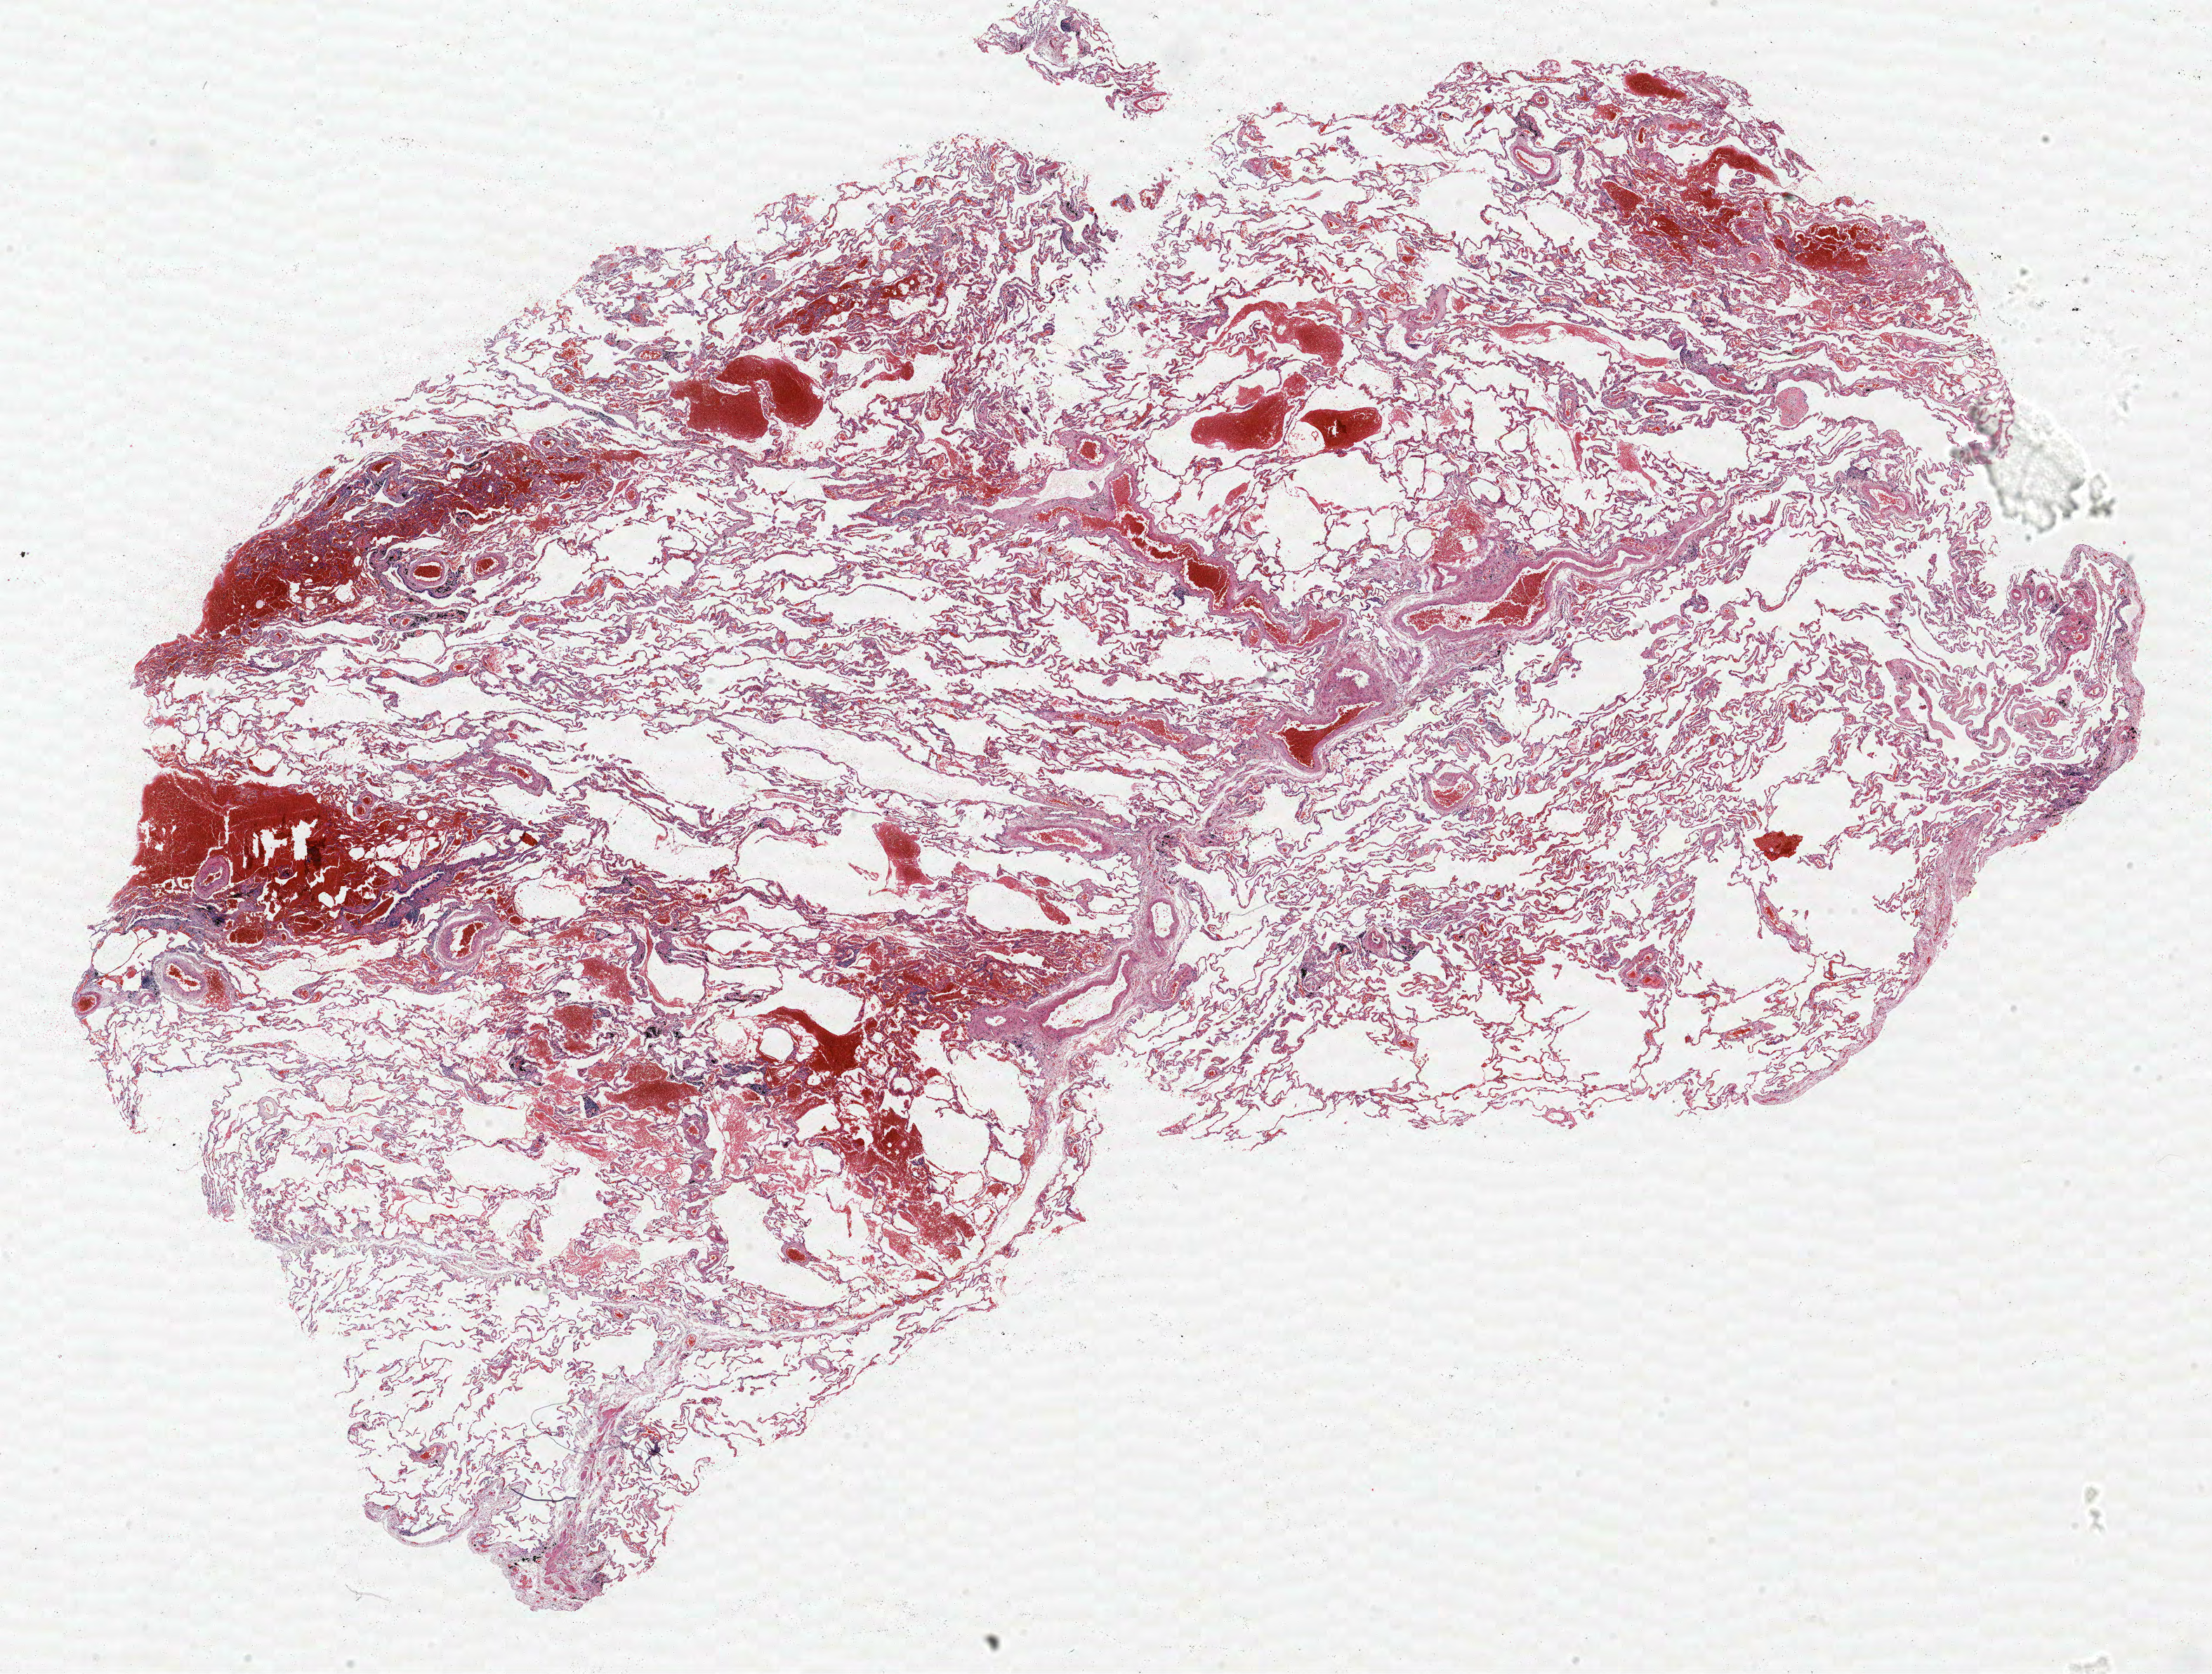
Whole-slide histology image, H&E-stained, shown as a low-resolution overview of the whole scanned area (about 25.2 x 19.1 mm). Formalin-fixed paraffin-embedded (FFPE) section. Lung tissue. Male, age 73 at enrolment. Former smoker at enrolment. Grade: poorly differentiated (G3).
Tumour size (pathology): 22 mm. Primary tumour location (clinical record): right upper lobe. Stage (AJCC 6th edition): IB. Participant's lung-cancer diagnosis: Adenocarcinoma, NOS. Note: participant had 2 primary lung cancers recorded; fields above describe the first.